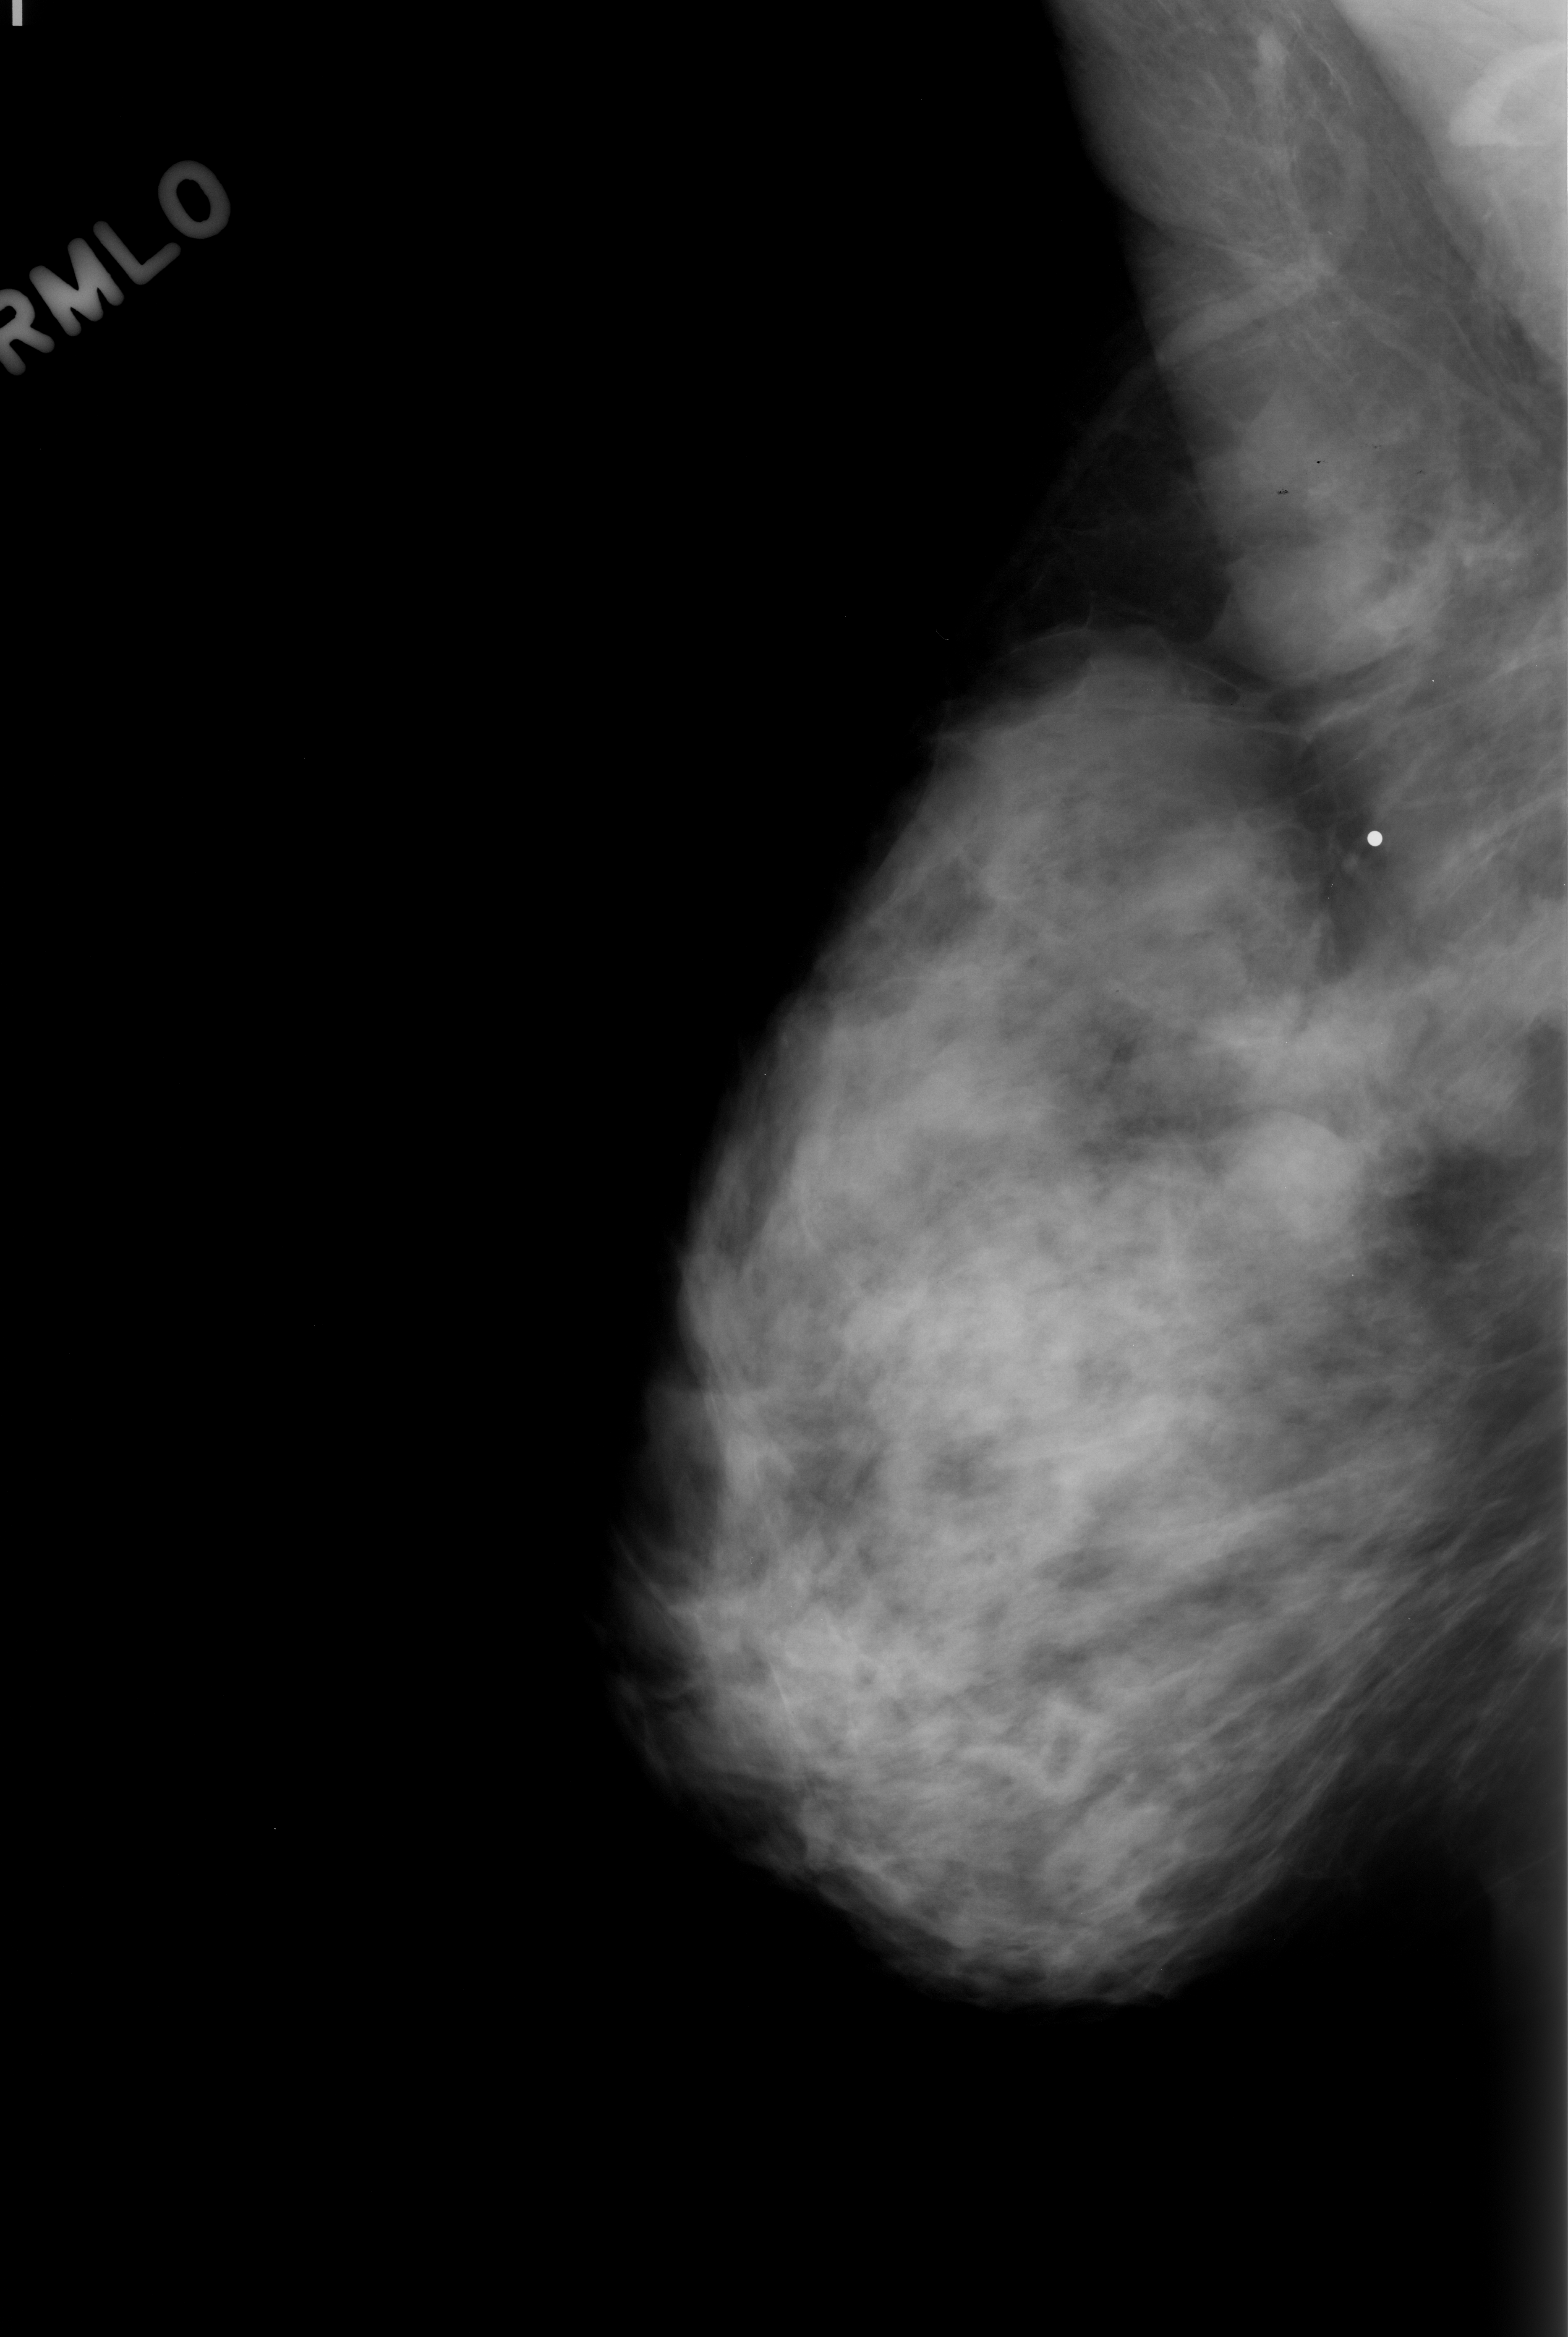
Mammogram (digitized film); right breast; MLO view; breast composition: heterogeneously dense (BI-RADS density category 3 of 4); 1568 × 2337 image matrix.
Expert-marked regions of interest on this image (one box per marked abnormality):
- mass, shape oval, margins obscured; BI-RADS assessment category 3; pathology (as recorded): benign: box from (x=1215, y=1111) to (x=1370, y=1259) px